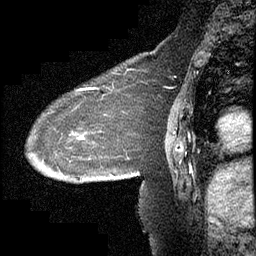
Breast MRI (dynamic contrast-enhanced), one sagittal slice; slice 144 of 232 in the series (ordered by position); dynamic contrast-enhanced study with each time point stored as its own series, time point 2 of 4 at this slice position (early post-contrast, ordered by acquisition time); 1.5 T; TE 4.2 ms, TR 6.7 ms; 256 × 256 image matrix. Female patient, age 63 years. Case-level facts recorded for this patient, not image findings: setting: breast cancer imaged before/during neoadjuvant chemotherapy; receptor status: triple-negative.
Annotated regions visible in this slice (semi-automatic segmentation, software-assisted and operator-edited):
- analysis volume of interest (the breast-tissue region the enhancement analysis was run in; not a lesion): bounding box <26,90,140,210> (left, top, right, bottom; pixels)
- tumour enhancement mask (voxels above the 70 % enhancement threshold inside the analysis volume of interest): <75,90,114,177>